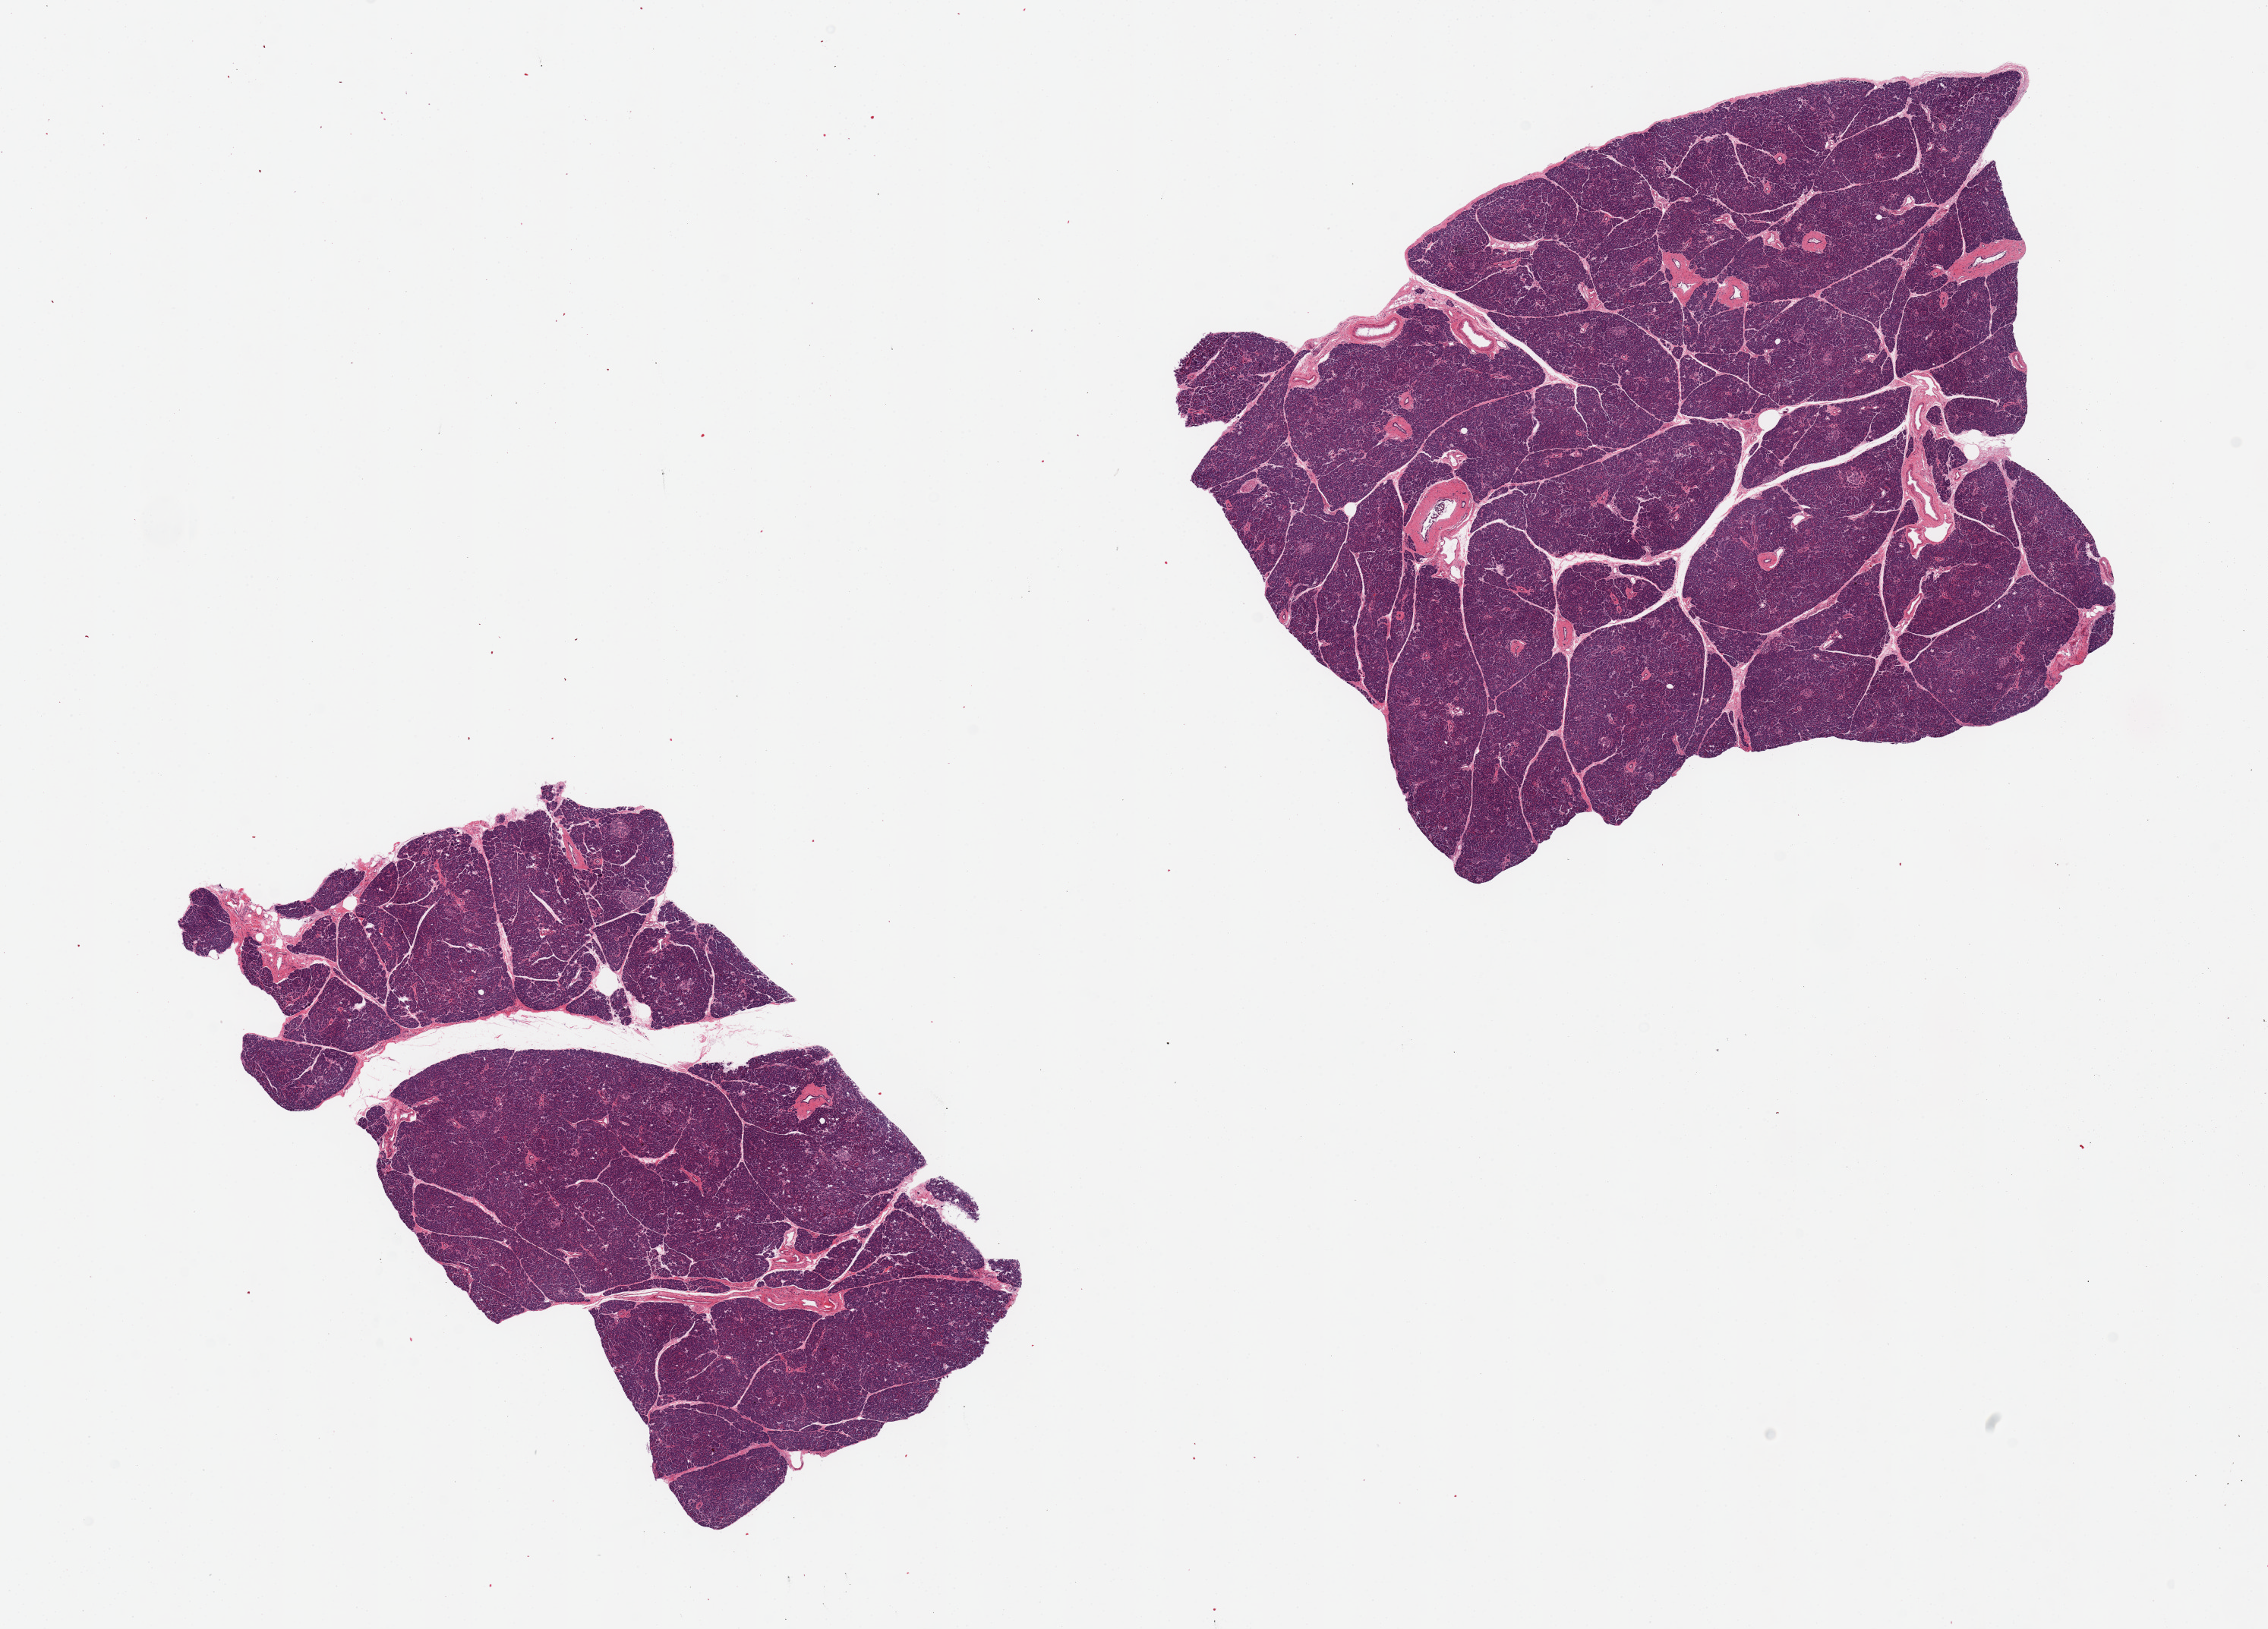
Haematoxylin and eosin whole-slide image, whole scanned area (about 23.6 x 17.0 mm) shown as a low-resolution overview. PAXgene-fixed, paraffin-embedded tissue. Section of pancreas (target tissue). Tissue donor sample. Donor sex: female.
* reviewer comment on this tissue sample: 2 pieces